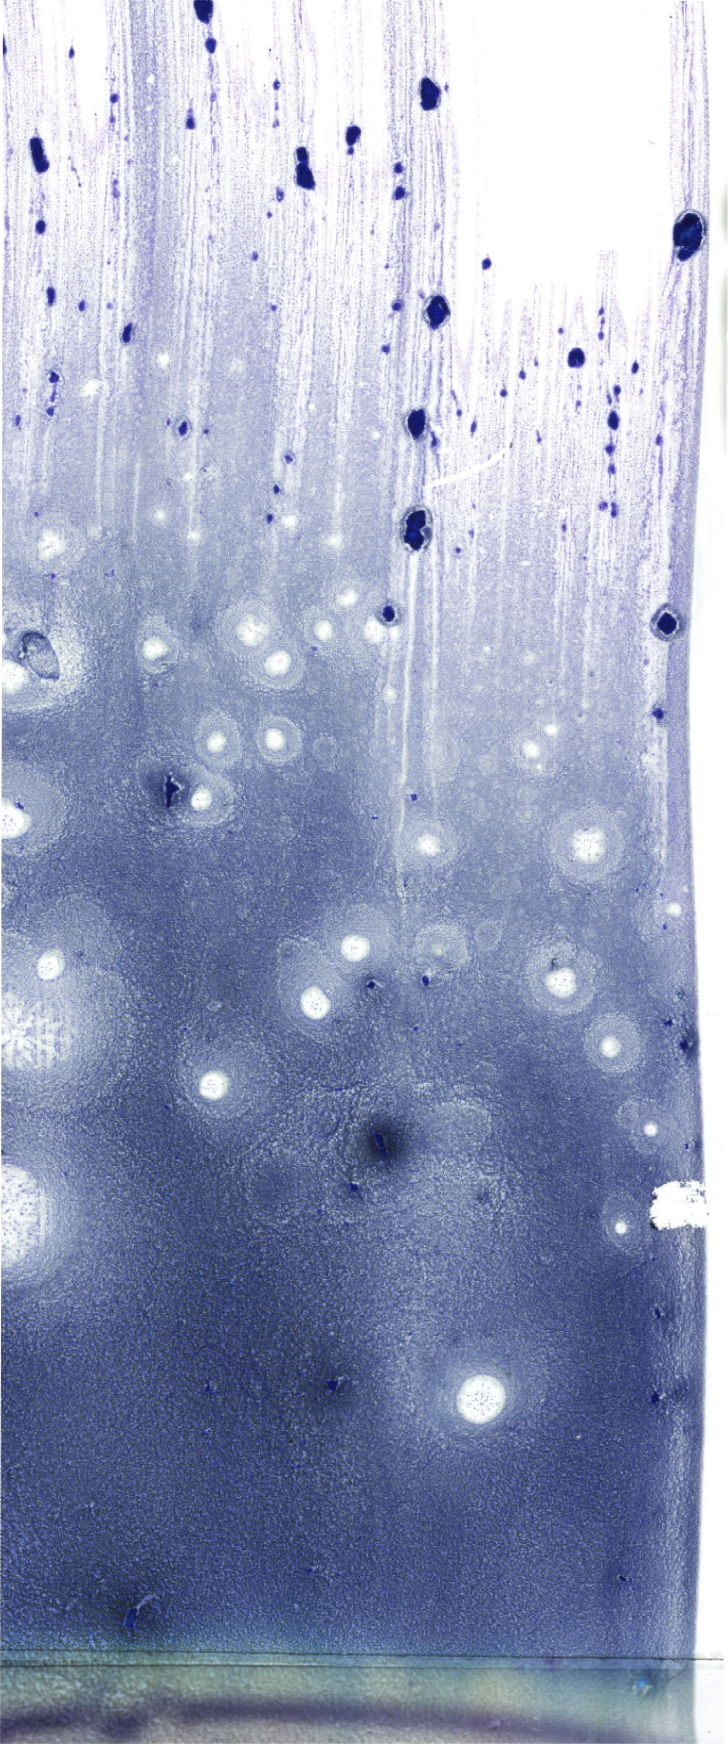
May-Grünwald-Giemsa (MGG)-stained marrow aspirate smear (whole slide) — shown as a low-resolution overview of the whole scanned area (about 20.6 x 49.4 mm). Female patient.
Diagnosis: Mixed Phenotype Acute Leukemia, B/Myeloid.